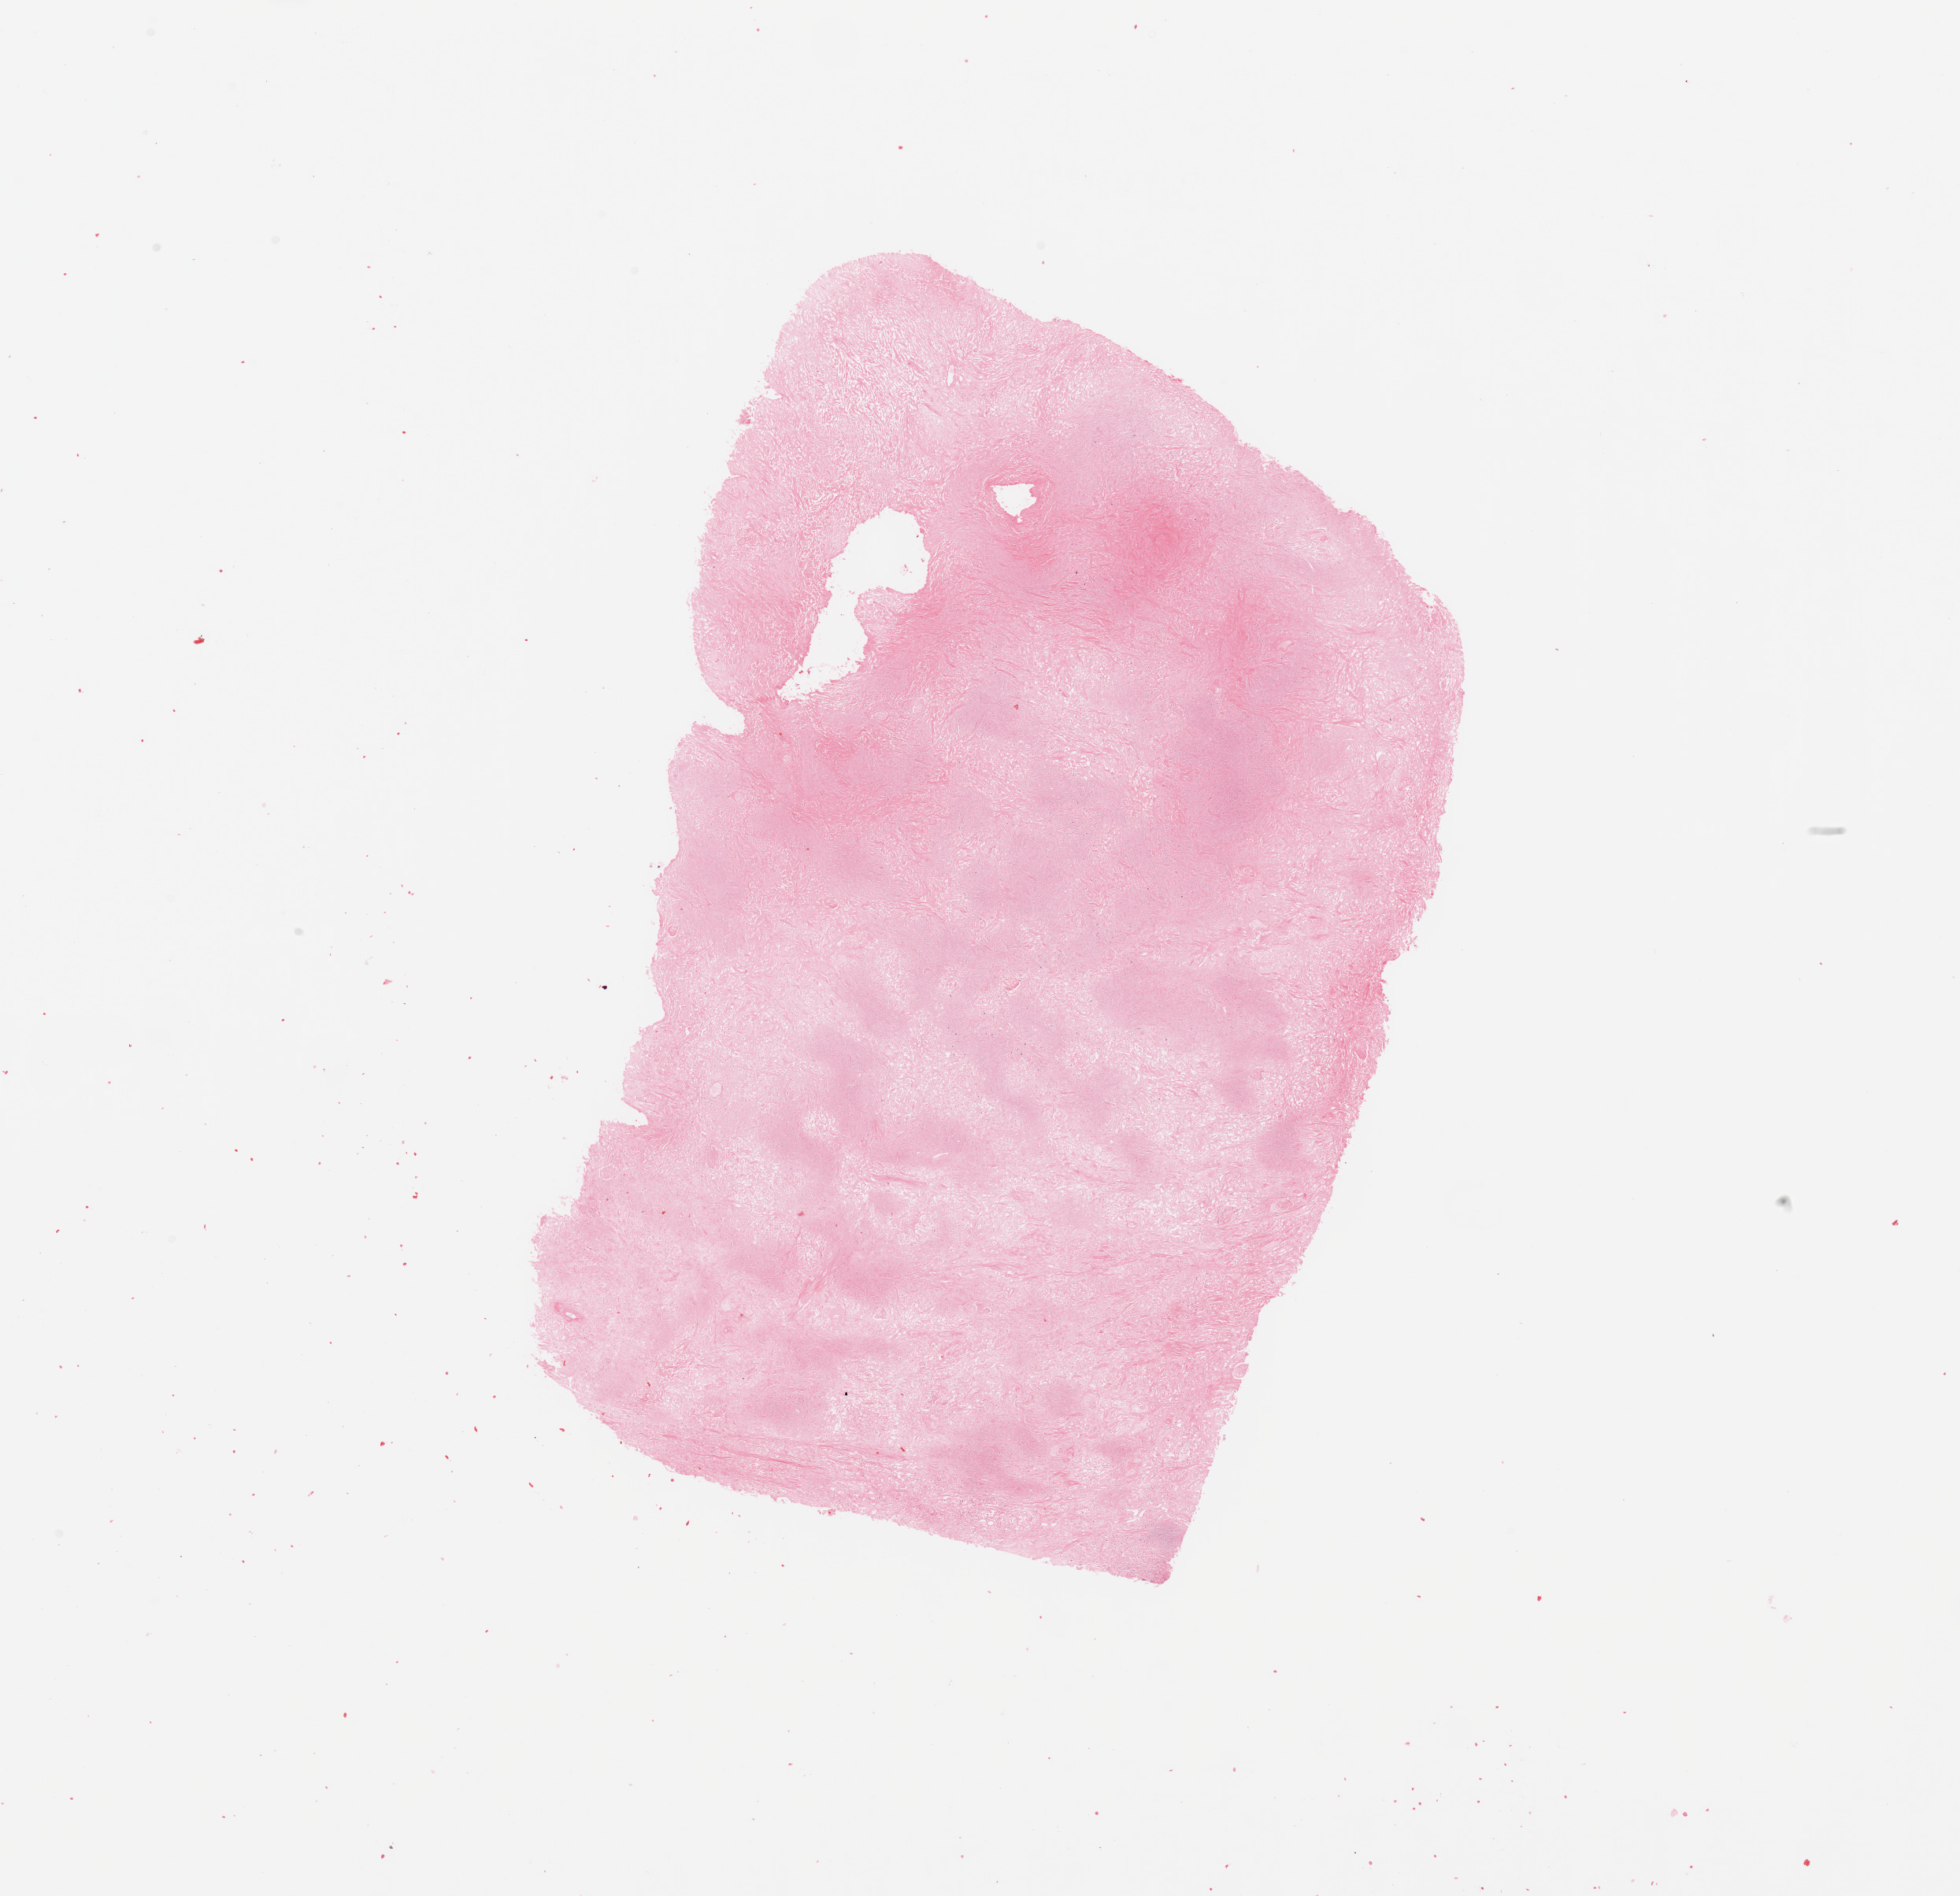
H&E-stained whole-slide image, shown as a low-resolution overview of the whole scanned area (about 19.7 x 19.0 mm); kidney, tumour tissue. Female, 68 y/o. Histologic grade: G3 (poorly differentiated).
* AJCC pathologic stage: IV
* histologic diagnosis: Renal cell carcinoma, NOS